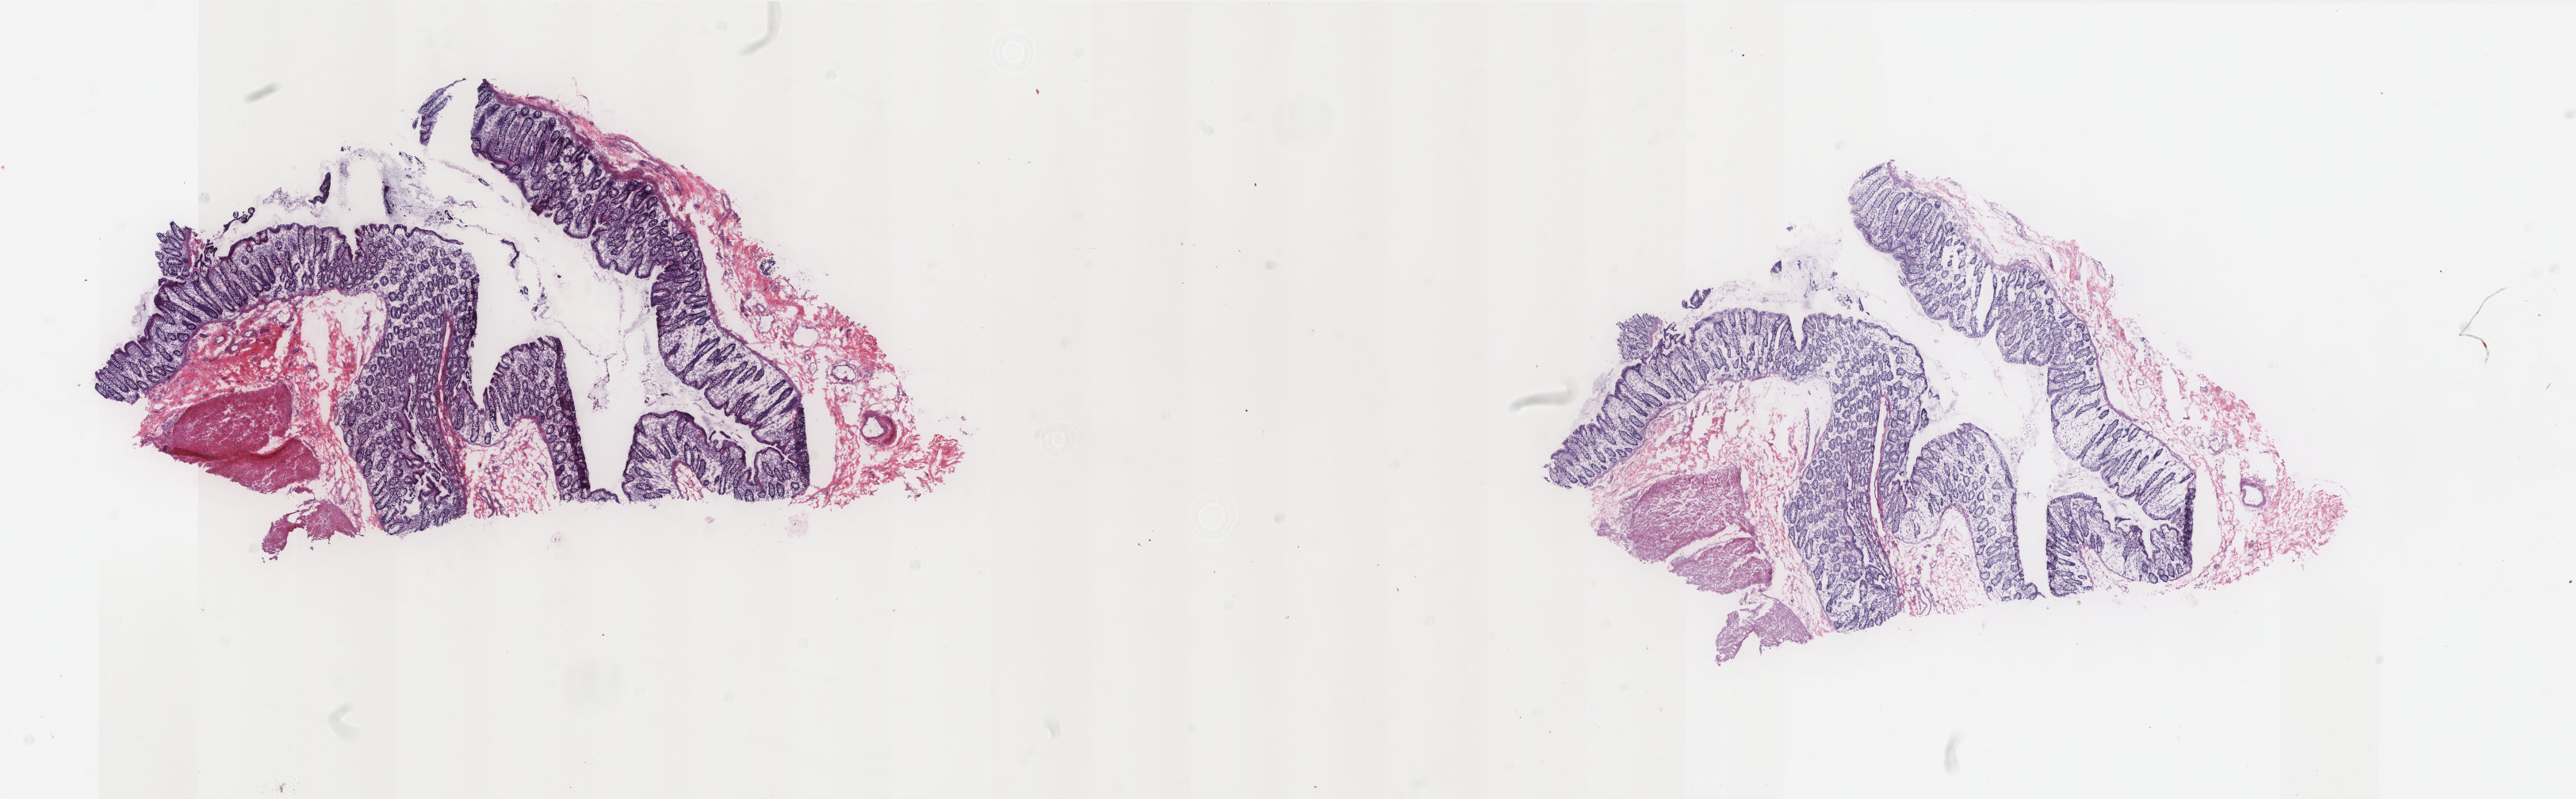
Digitized H&E-stained tissue section (whole slide), low-resolution overview of the scanned area, about 25.9 x 8.1 mm, frozen section, rectum, solid tissue normal (non-tumour tissue) sample. Male patient; age at initial diagnosis 71 years.
This section: solid tissue normal sample (biorepository sample class). Patient diagnosis: Adenocarcinoma, NOS.